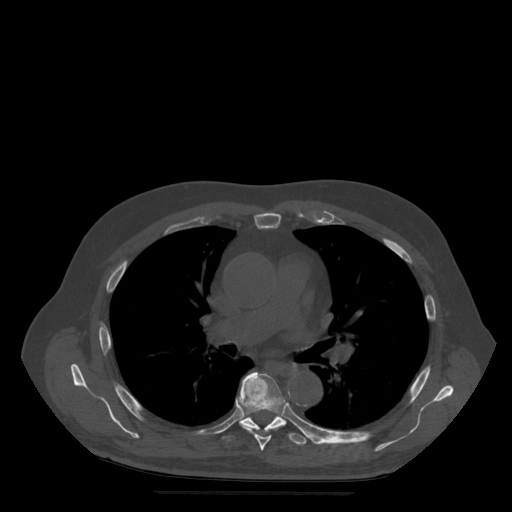
CT including the spine, one axial slice; slice 345 of 522 in the series (ordered by position); bone window (W 1800 / L 400 HU); 1.25 mm slice thickness; 512 × 512 image matrix, field of view 420 × 420 mm. Patient age 72 years. Case-level facts recorded for this patient, not image findings: primary cancer: prostate.
Structures marked on this image (semi-automatic segmentation, software-assisted and operator-edited):
- T6 vertebra: bounding box [x1, y1, x2, y2] px = [238, 372, 286, 451]
- T7 vertebra: [222, 416, 309, 446]